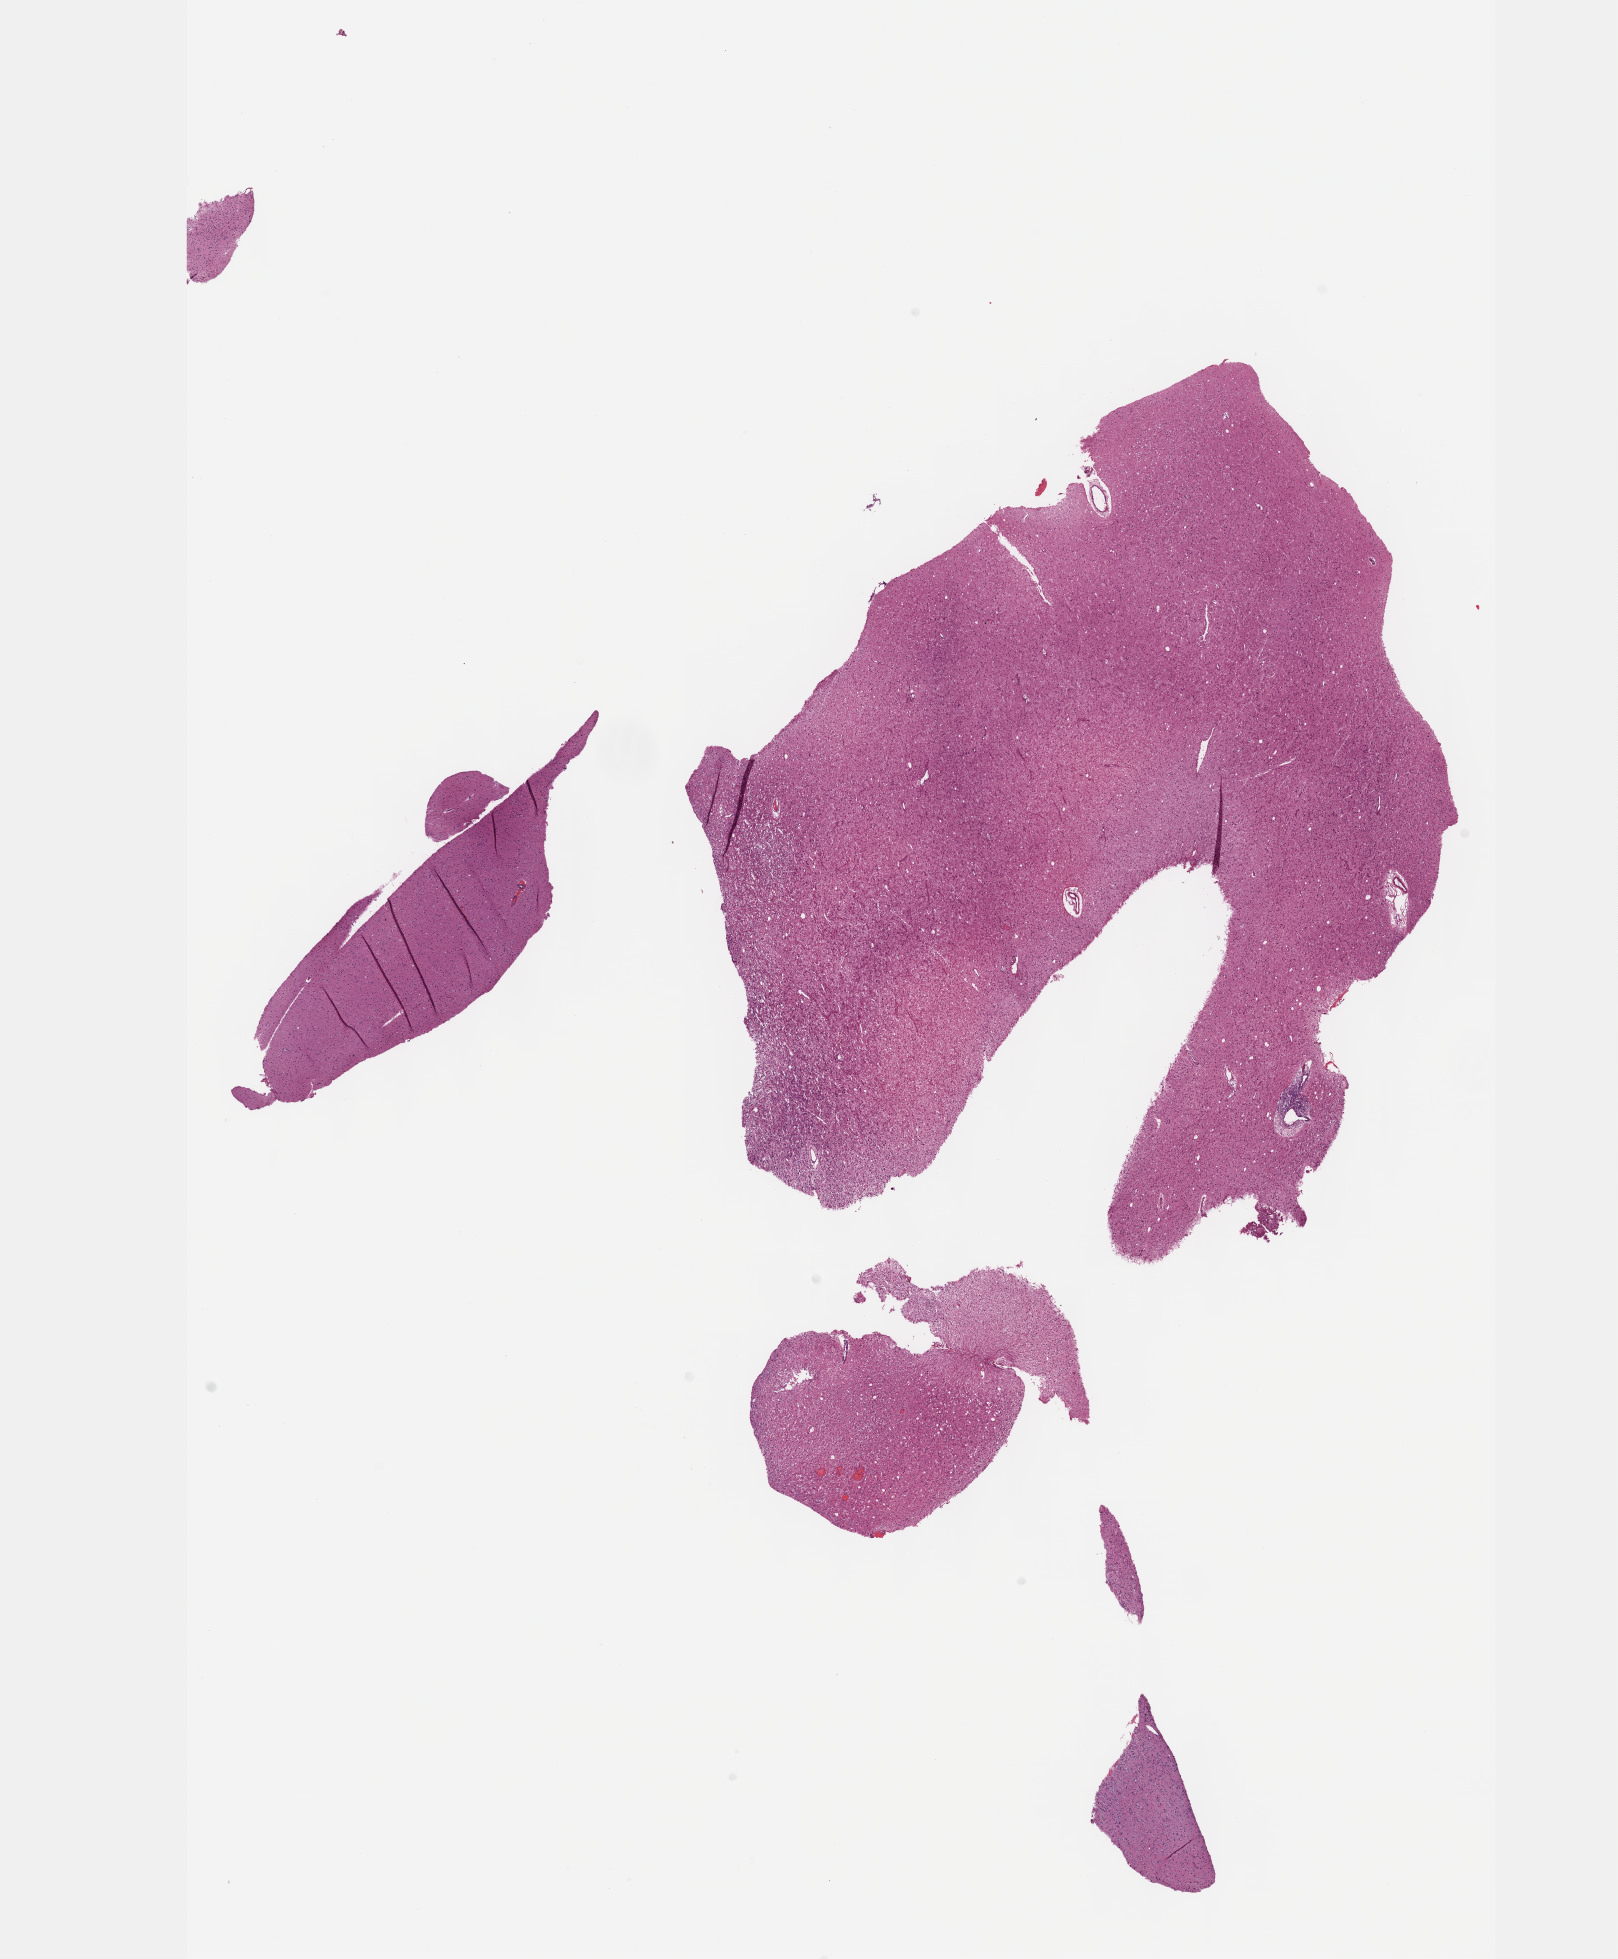
H&E whole-slide image, a low-resolution overview of the entire scanned area, about 13.1 x 15.8 mm; formalin-fixed paraffin-embedded (FFPE) diagnostic section; primary tumour sample from the brain. Patient: female, age at initial diagnosis 29 years. Histologic grade: G2 (moderately differentiated).
- histologic diagnosis: Oligodendroglioma, NOS